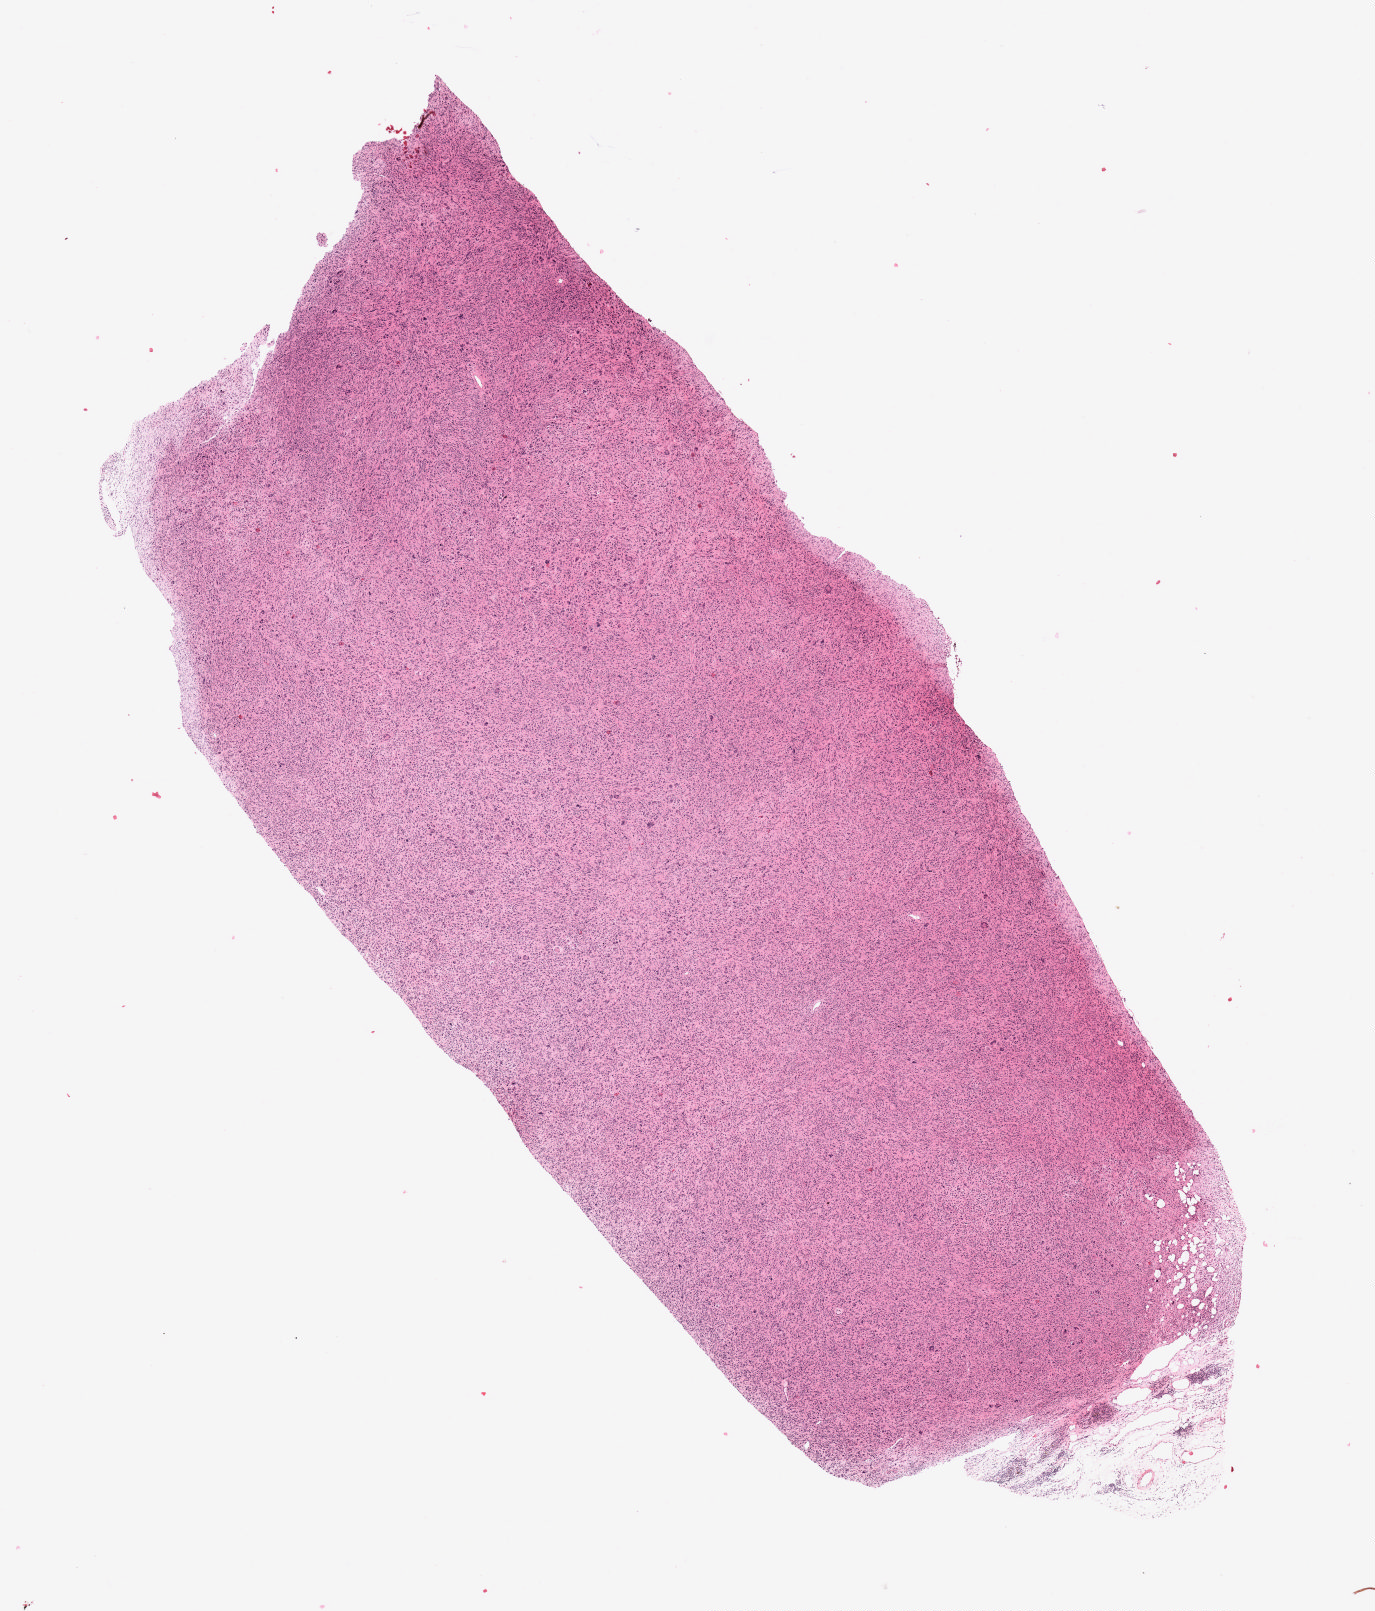
Digitized H&E tissue section (whole slide), whole scanned area (about 11.0 x 12.9 mm) shown as a low-resolution overview; formalin-fixed paraffin-embedded (FFPE) diagnostic section; primary tumour sample from the retroperitoneum and peritoneum. Male, age 63 years at initial diagnosis.
Histologic diagnosis: Leiomyosarcoma, NOS (retroperitoneum).